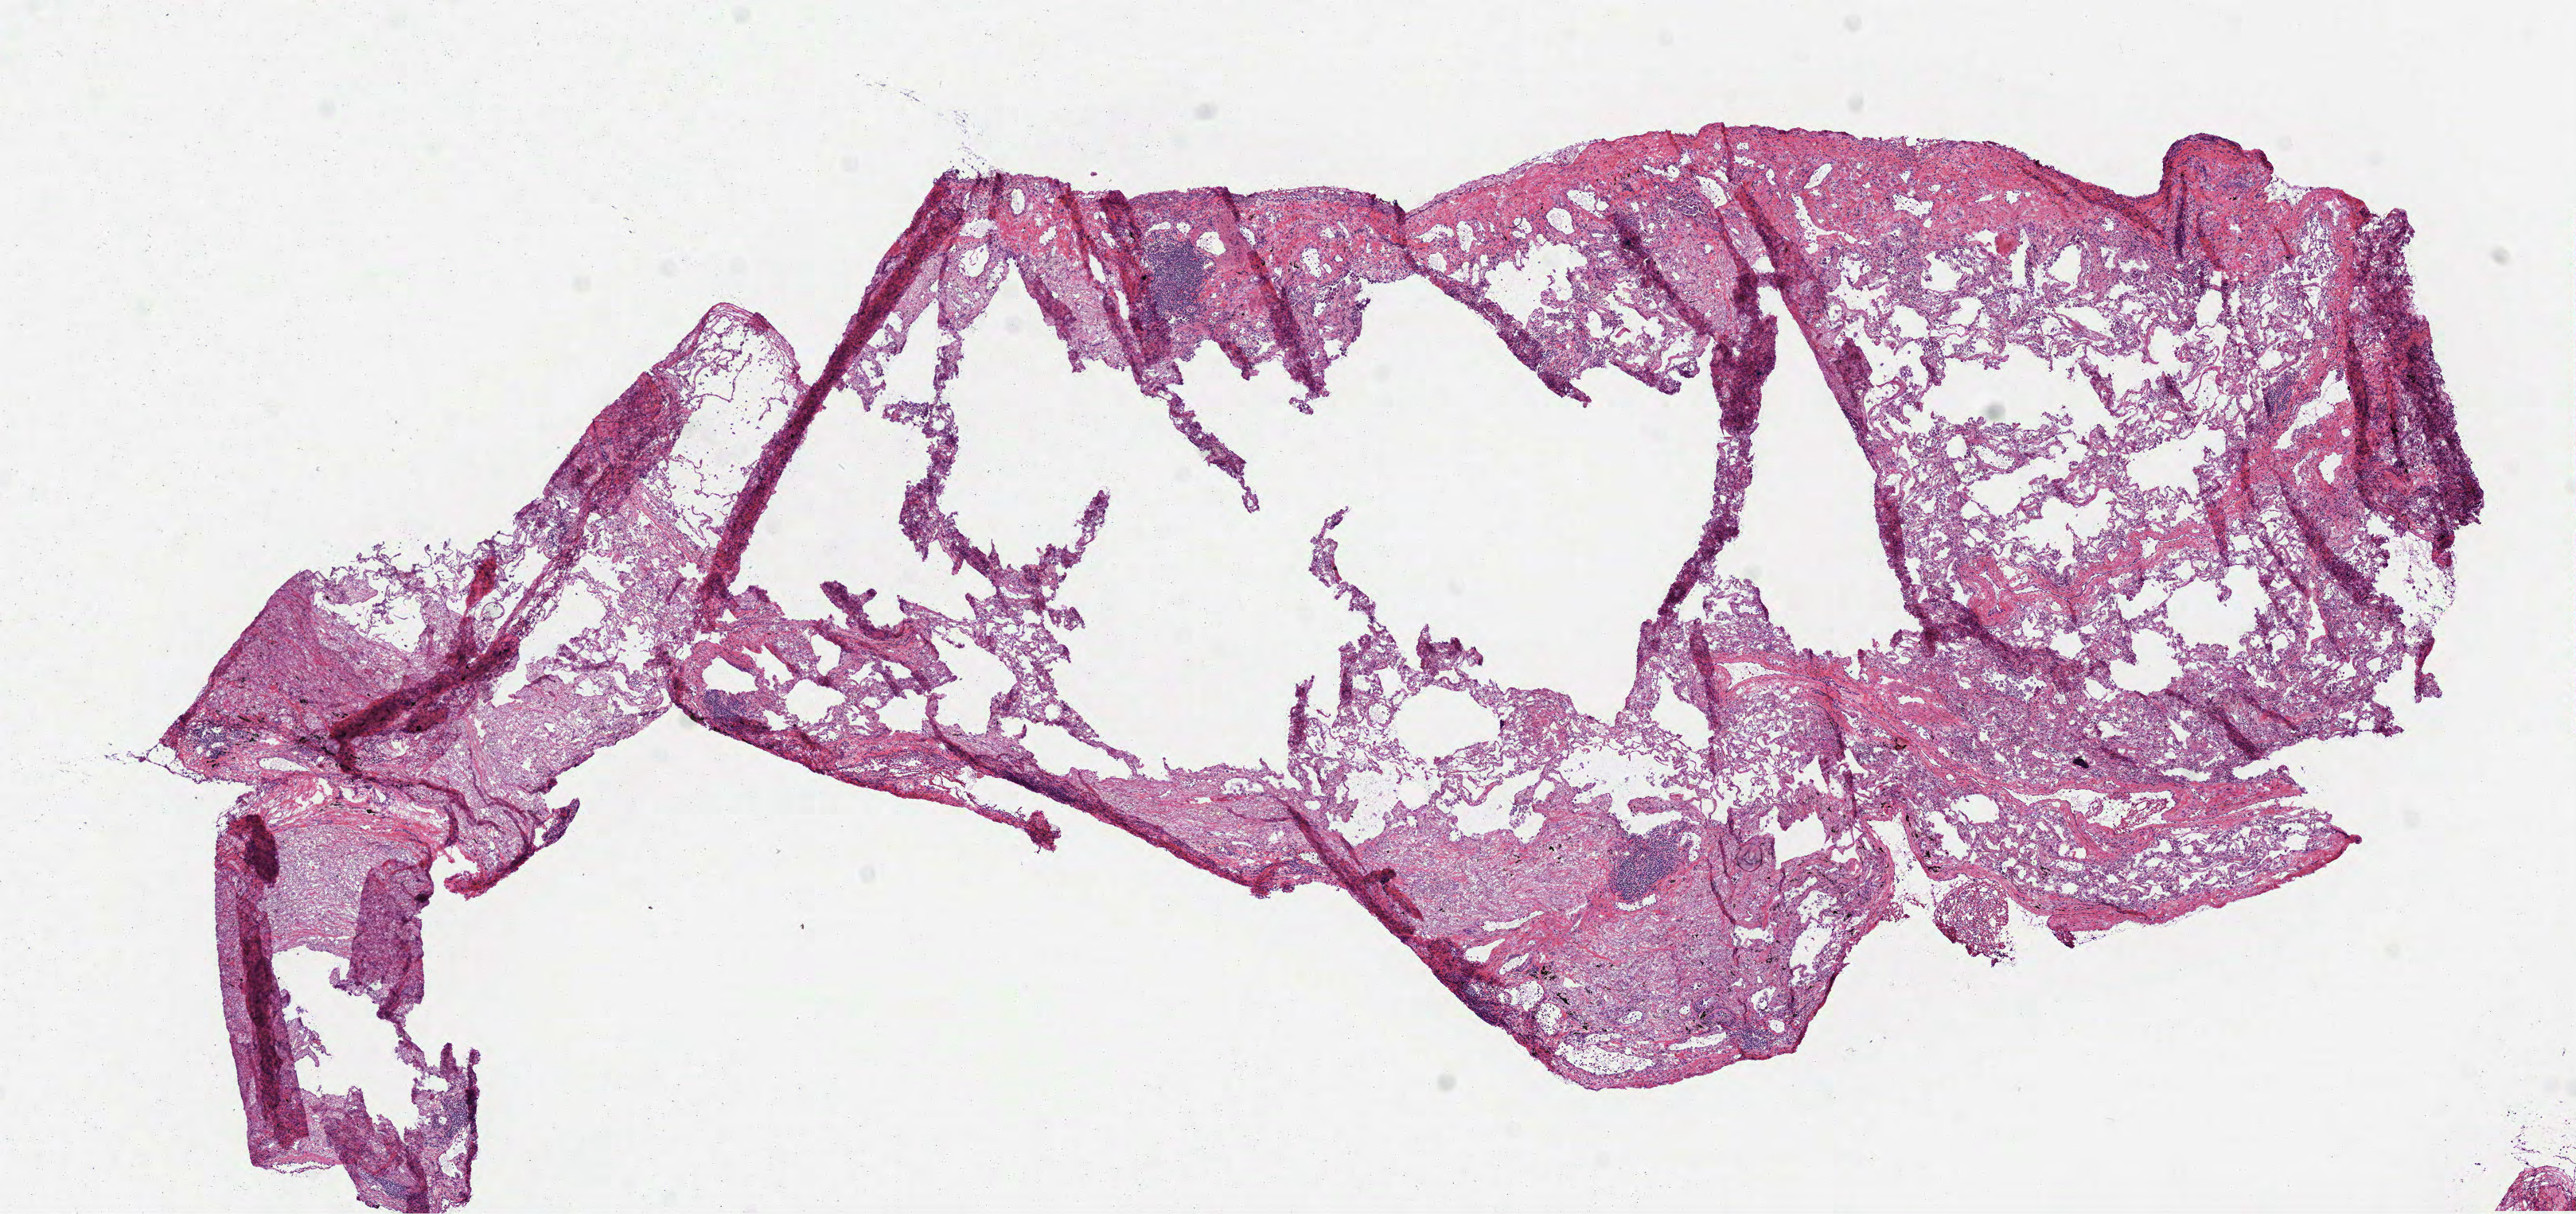
Digitized Hematoxylin and eosin (H&E) stained tissue section (whole slide) — low-resolution overview of the scanned area, about 13.1 x 6.2 mm, frozen section from the top of the tissue portion, sample: solid tissue normal (non-tumour tissue), lung. Patient: male, age at initial diagnosis 73 years. Infiltration values recorded for this section: lymphocyte infiltration 10%, monocyte infiltration 20%, neutrophil infiltration 10%.
This section: solid tissue normal sample (biorepository sample class). Patient diagnosis: Squamous cell carcinoma, NOS (upper lobe, lung).